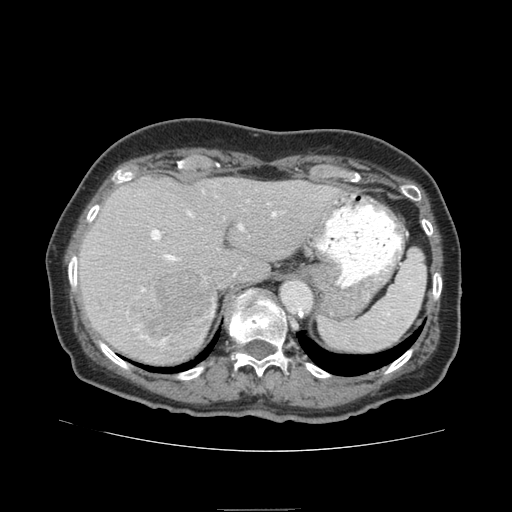
Contrast-enhanced abdominal CT (liver protocol), one axial slice. Position 59 of 95 along the scan axis. 140 kVp. Soft-tissue window (W 400 / L 40 HU). 512 × 512 image matrix, field of view 360 × 360 mm. From the clinical record (not read from this slice): diagnosis: hepatocellular carcinoma (patient treated with transarterial chemoembolisation; whether this scan precedes or follows treatment is not stated here); TNM stage (as recorded): Stage-IVA; Child-Pugh class: B; tumour nodularity: uninodular.
Structures marked on this image (semi-automatically segmented with operator editing):
- liver parenchyma outside the tumour (the mass and vessels are separate outlines, so this box may not span the whole liver): bounding box [x1, y1, x2, y2] px = [78, 176, 344, 364]
- mass: [130, 271, 217, 357]
- liver vessels: [135, 211, 277, 337]